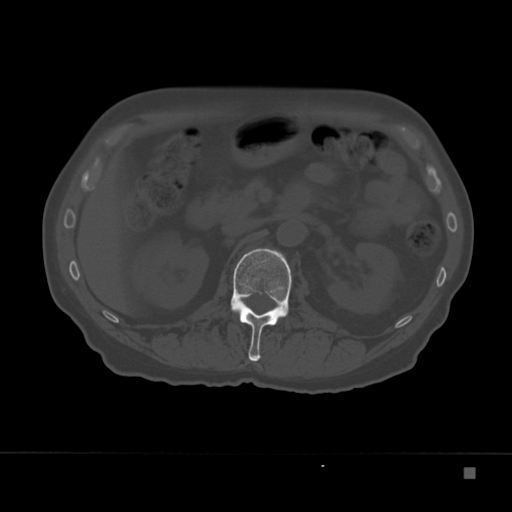
CT including the spine, one axial slice. Position 108 of 332 along the scan axis. 120 kVp. Bone window (W 1800 / L 400 HU). 1.5 mm slice thickness. 512 × 512 image matrix, field of view 389 × 389 mm. Patient: male, 72 years. Case-level facts recorded for this patient, not image findings: primary cancer: skeletal.
Outlined on this slice (semi-automatically segmented with operator editing):
- L1 vertebra: box from (x=230, y=248) to (x=292, y=362) px